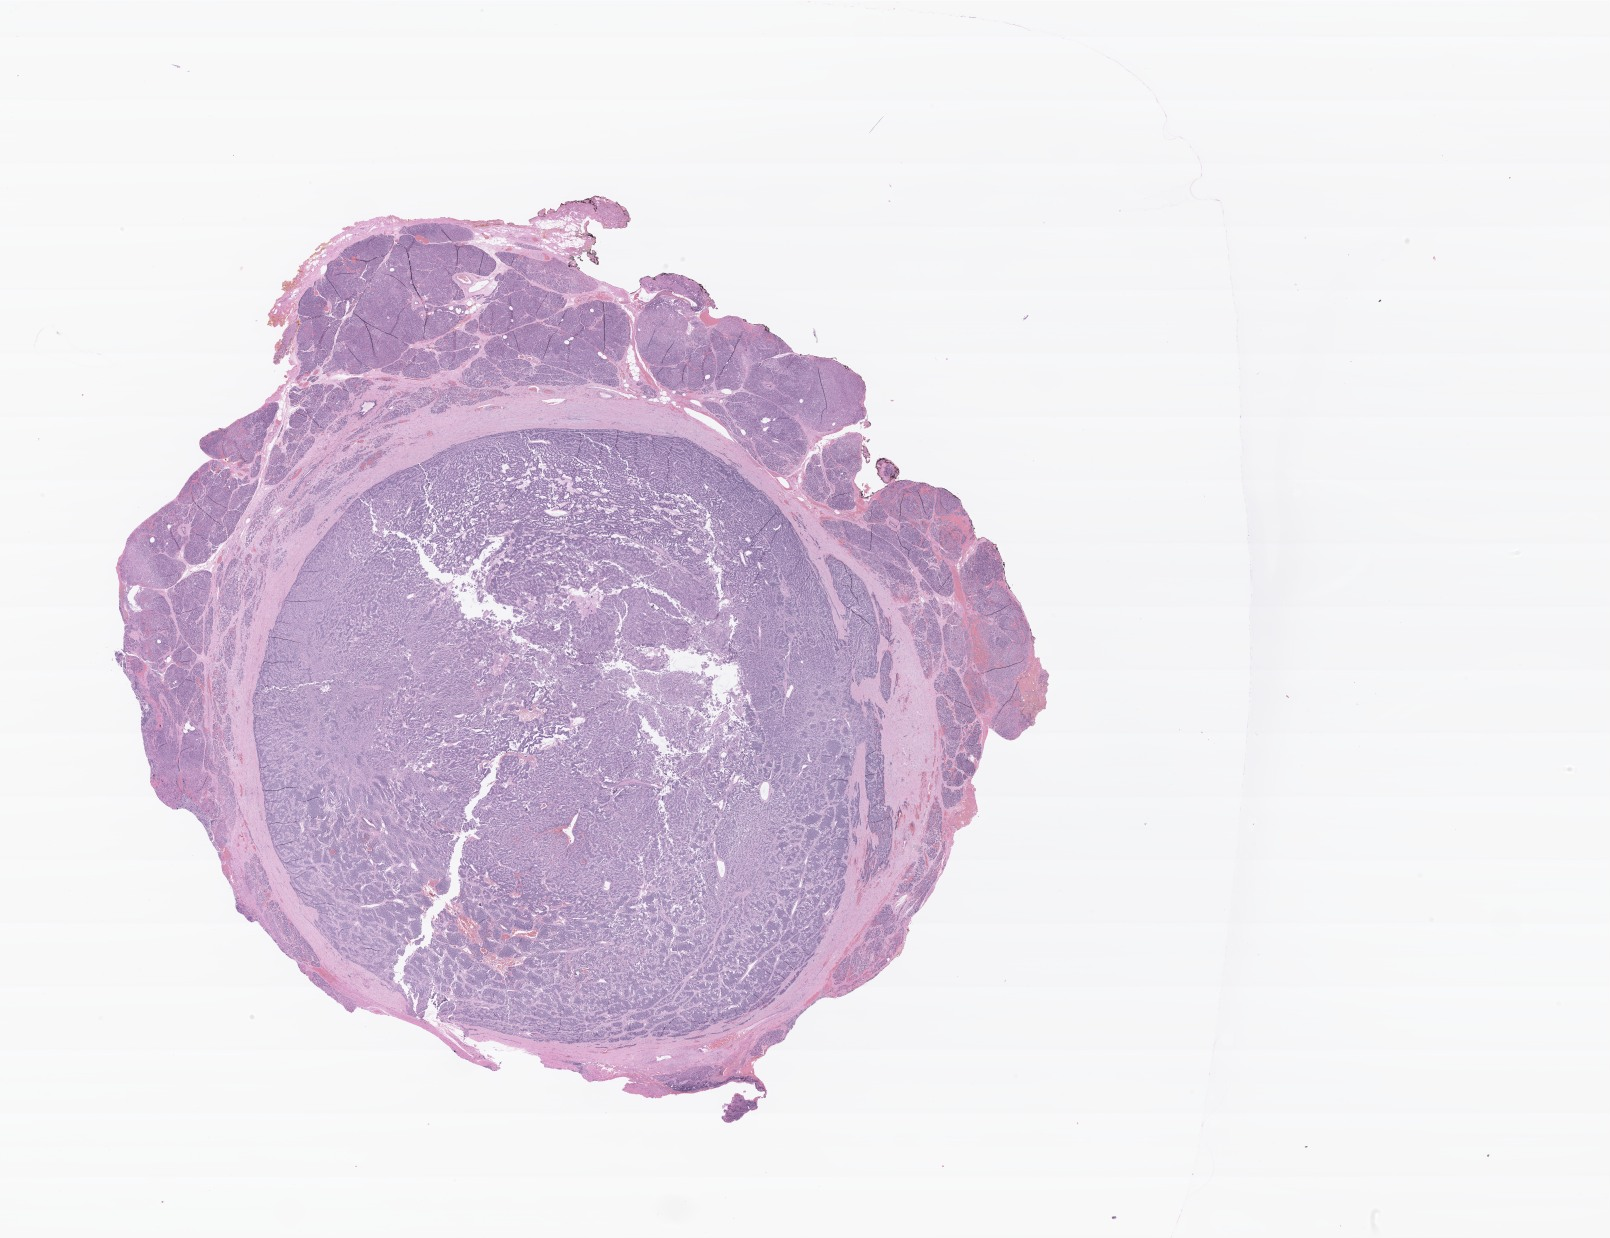
Digitized hematoxylin and eosin (H&E)-stained section of tumor tissue from the pancreas — a low-resolution overview of the entire scanned area, about 27.1 x 20.8 mm, formalin-fixed, paraffin-embedded (FFPE) tissue. Patient: female, age 228 months (19 years).
Diagnosis (ICD-O-3 morphology term): Neuroendocrine carcinoma, NOS.